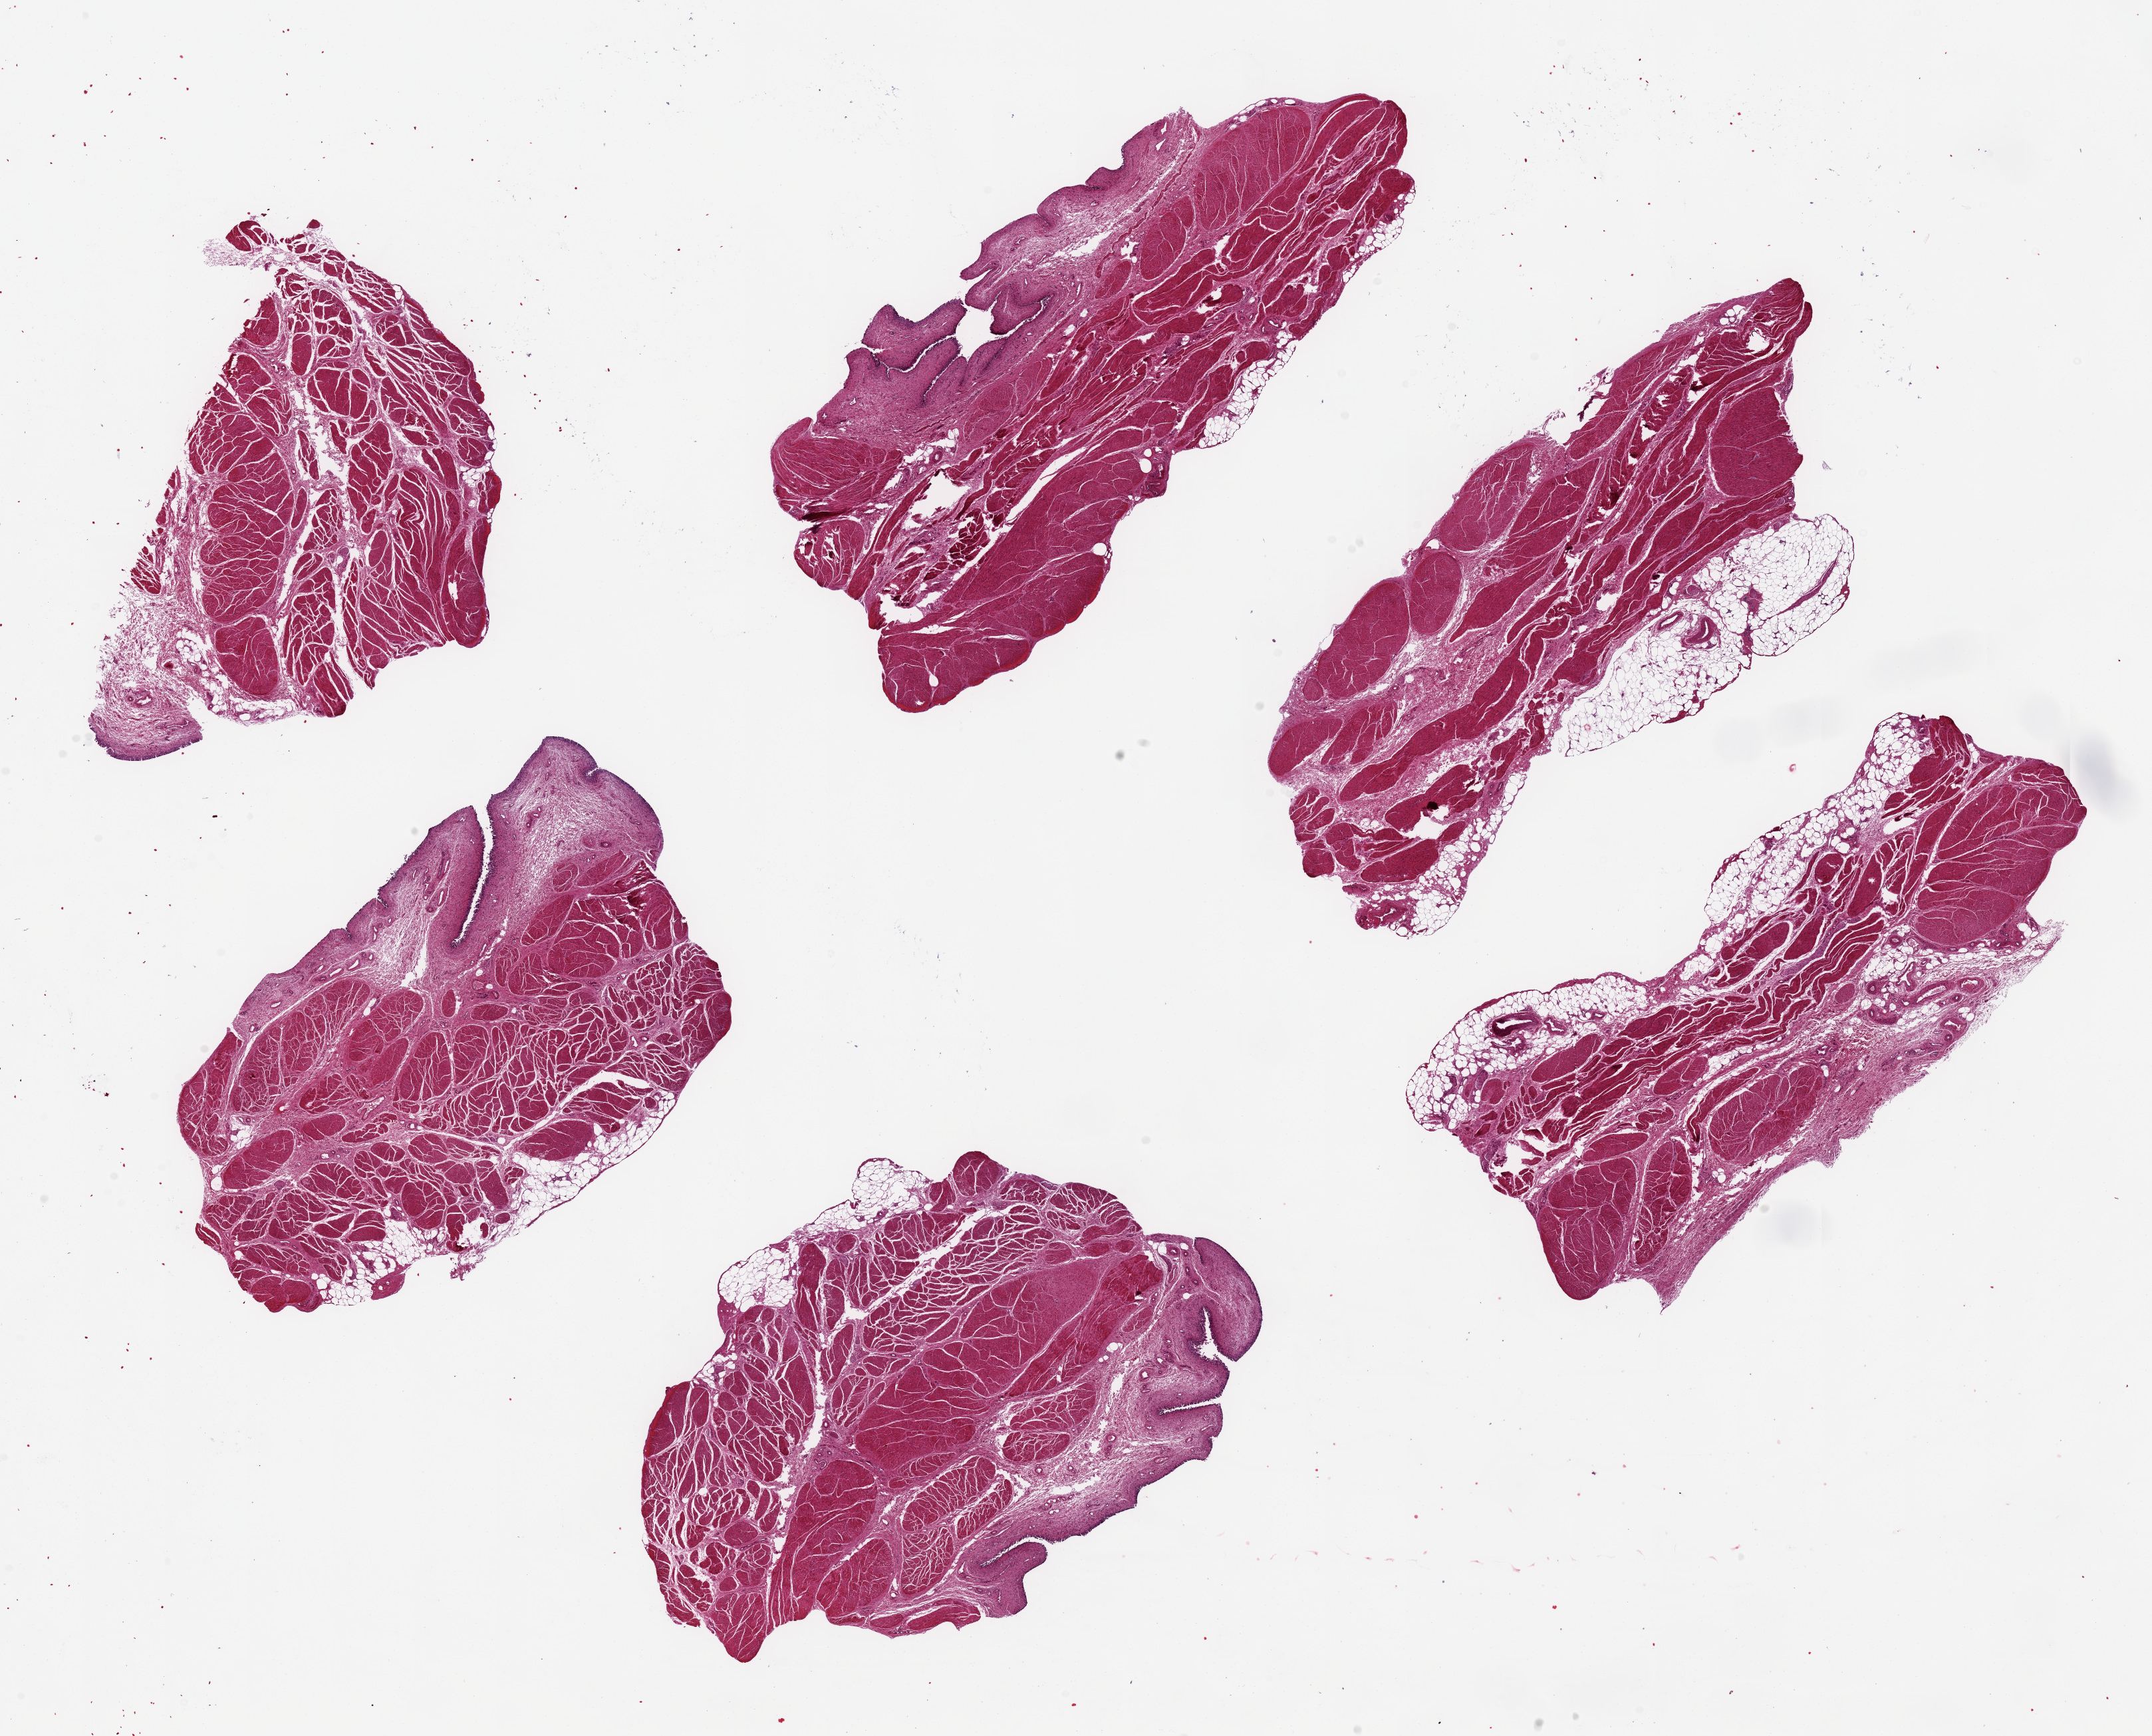
Digitized H&E-stained section, shown as a low-resolution overview of the whole scanned area (about 25.6 x 20.6 mm, acquisition: 20x scan); PAXgene-fixed, paraffin-embedded tissue; target tissue: urinary bladder; tissue donor sample. Donor: male.
Review note (as recorded): 6 ~ 8x3.5mm pieces. Urothelium completely sloughed; detrussor muscle and fat only.